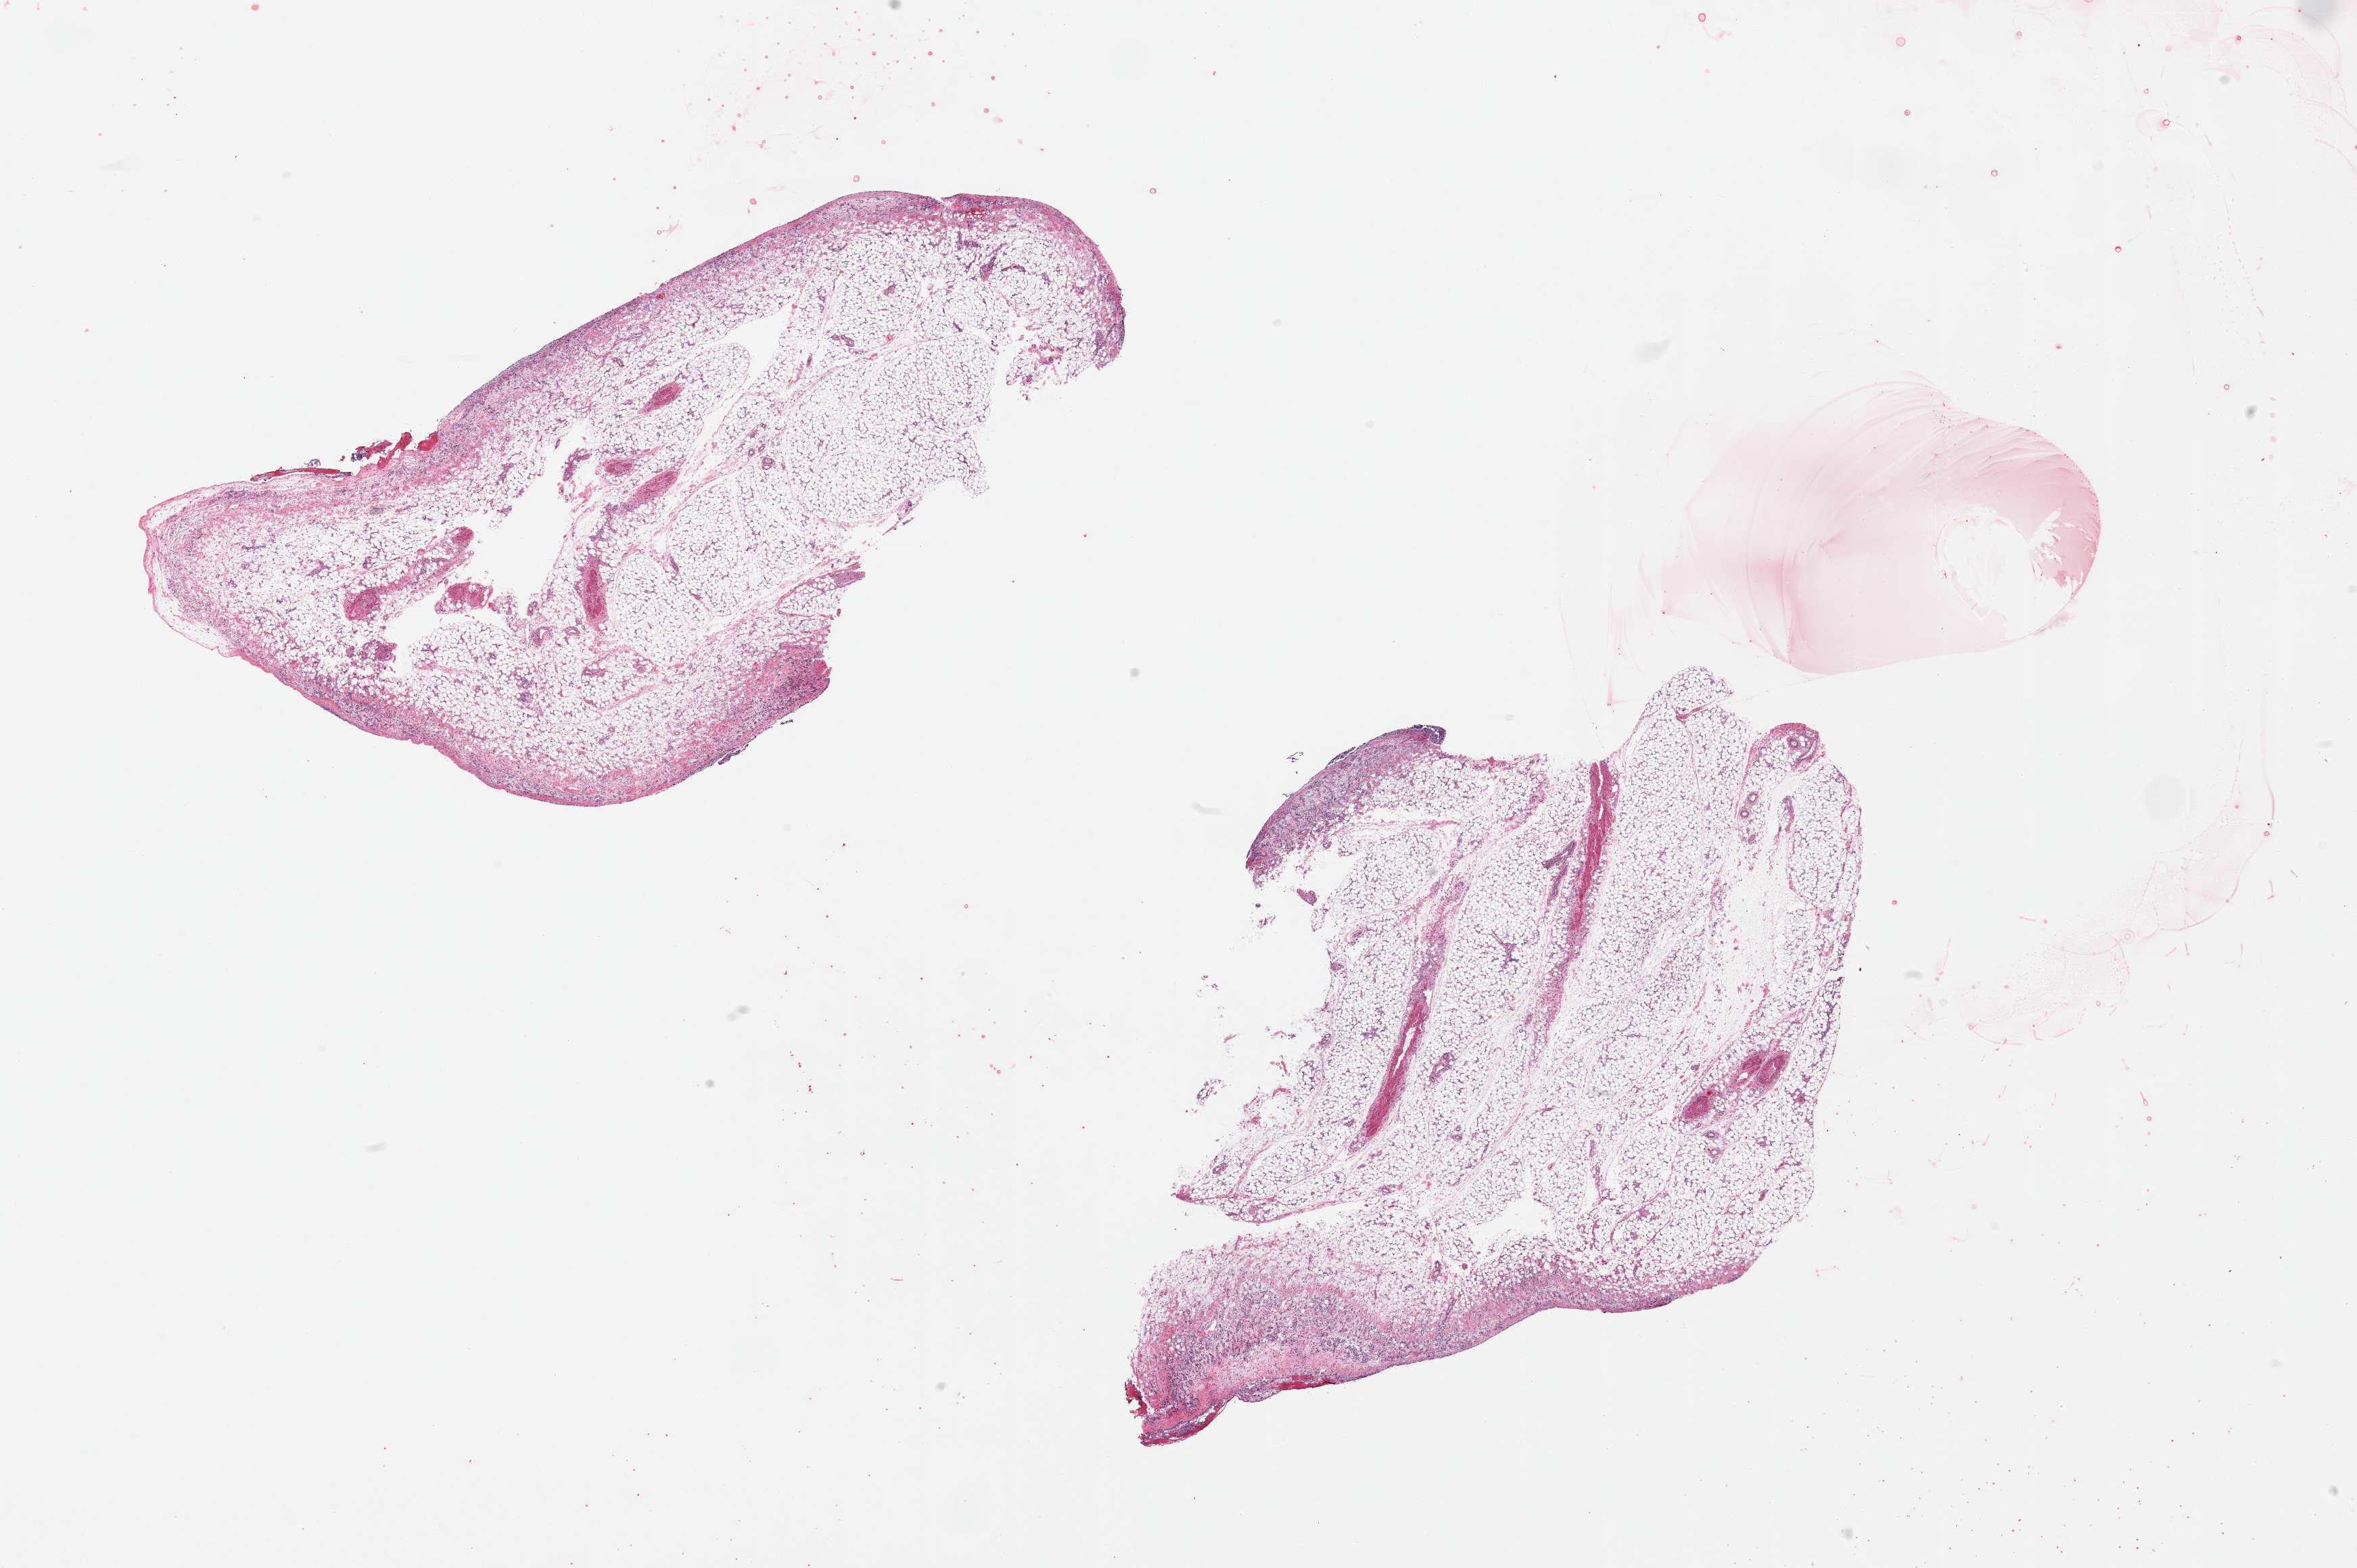
Haematoxylin and eosin whole-slide image, whole scanned area (about 27.6 x 18.3 mm, slide scanned at 20x) shown as a low-resolution overview; PAXgene-fixed, paraffin-embedded tissue; sampled site (target tissue): omentum; donor tissue sample. Donor sex: male.
Reviewer comment on this tissue sample: 2 pieces, 5-10% vascular/mesothelial tissue.